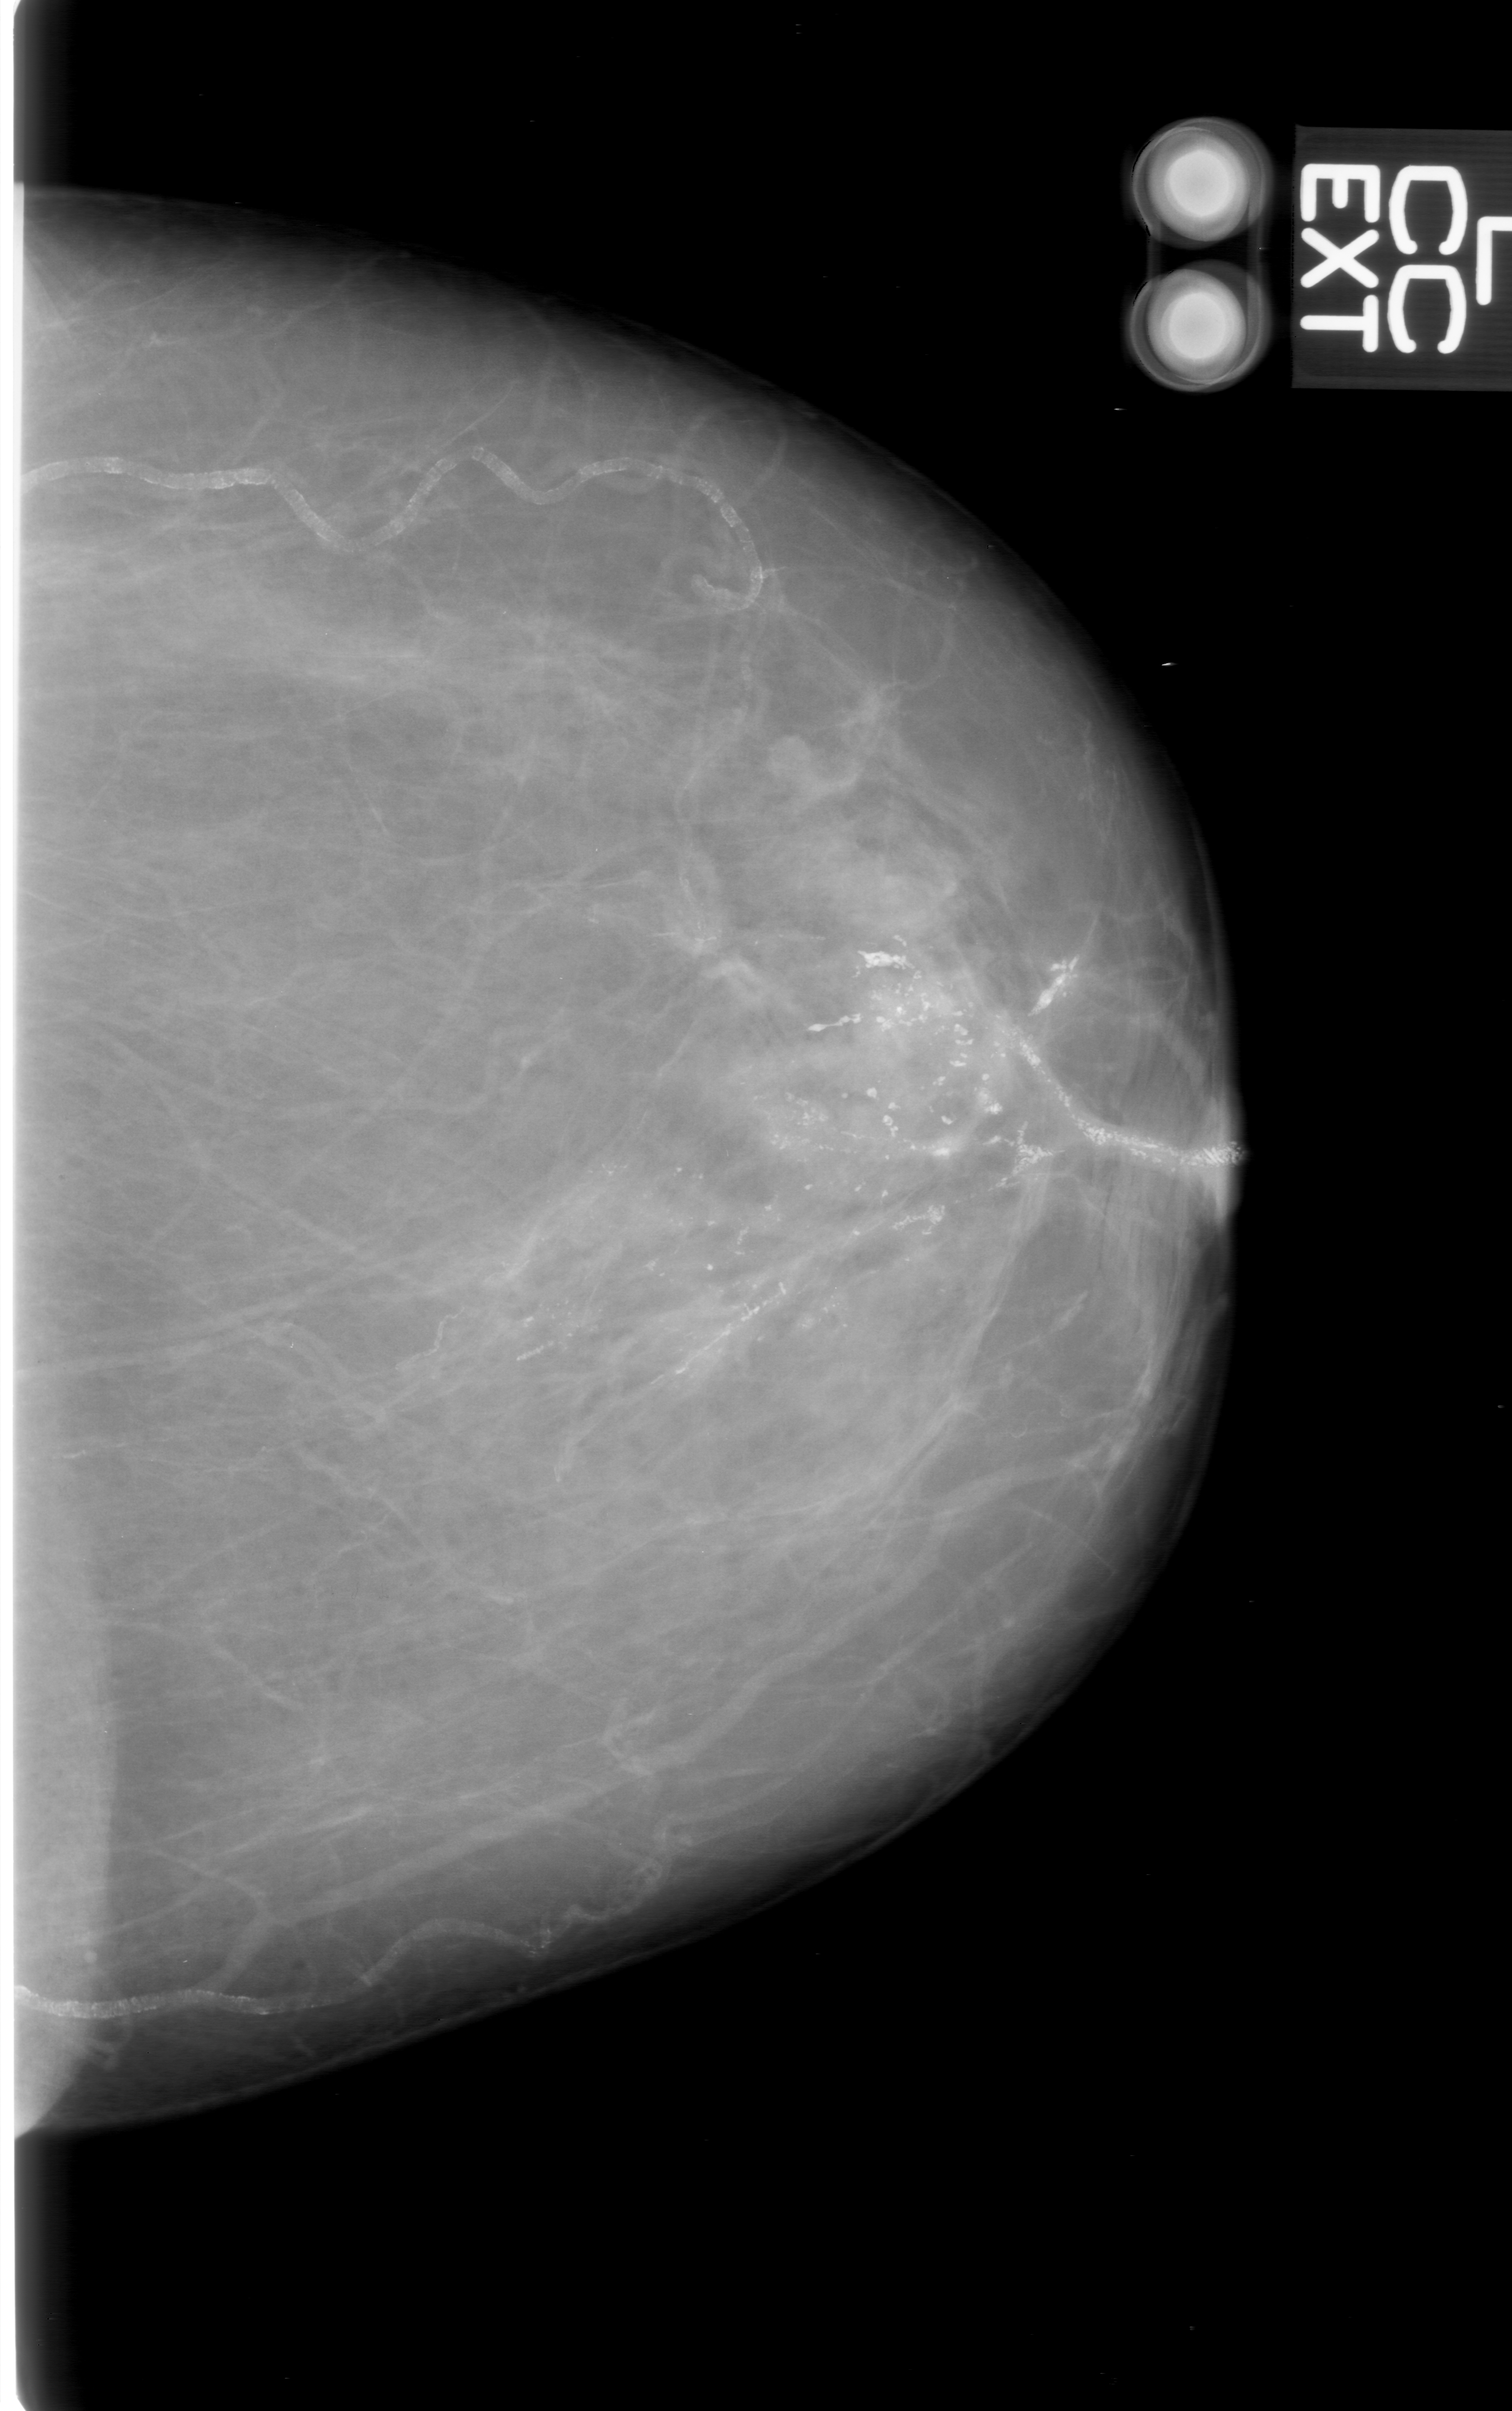
Digitized screen-film mammogram; left breast; craniocaudal (CC) view; breast composition: almost entirely fatty (BI-RADS density category 1 of 4).
- Abnormality record for this image: calcifications, morphology pleomorphic, distribution linear; BI-RADS assessment category 5; subtlety rating 5 on a 1 (subtle) to 5 (obvious) scale; pathology (as recorded): malignant.